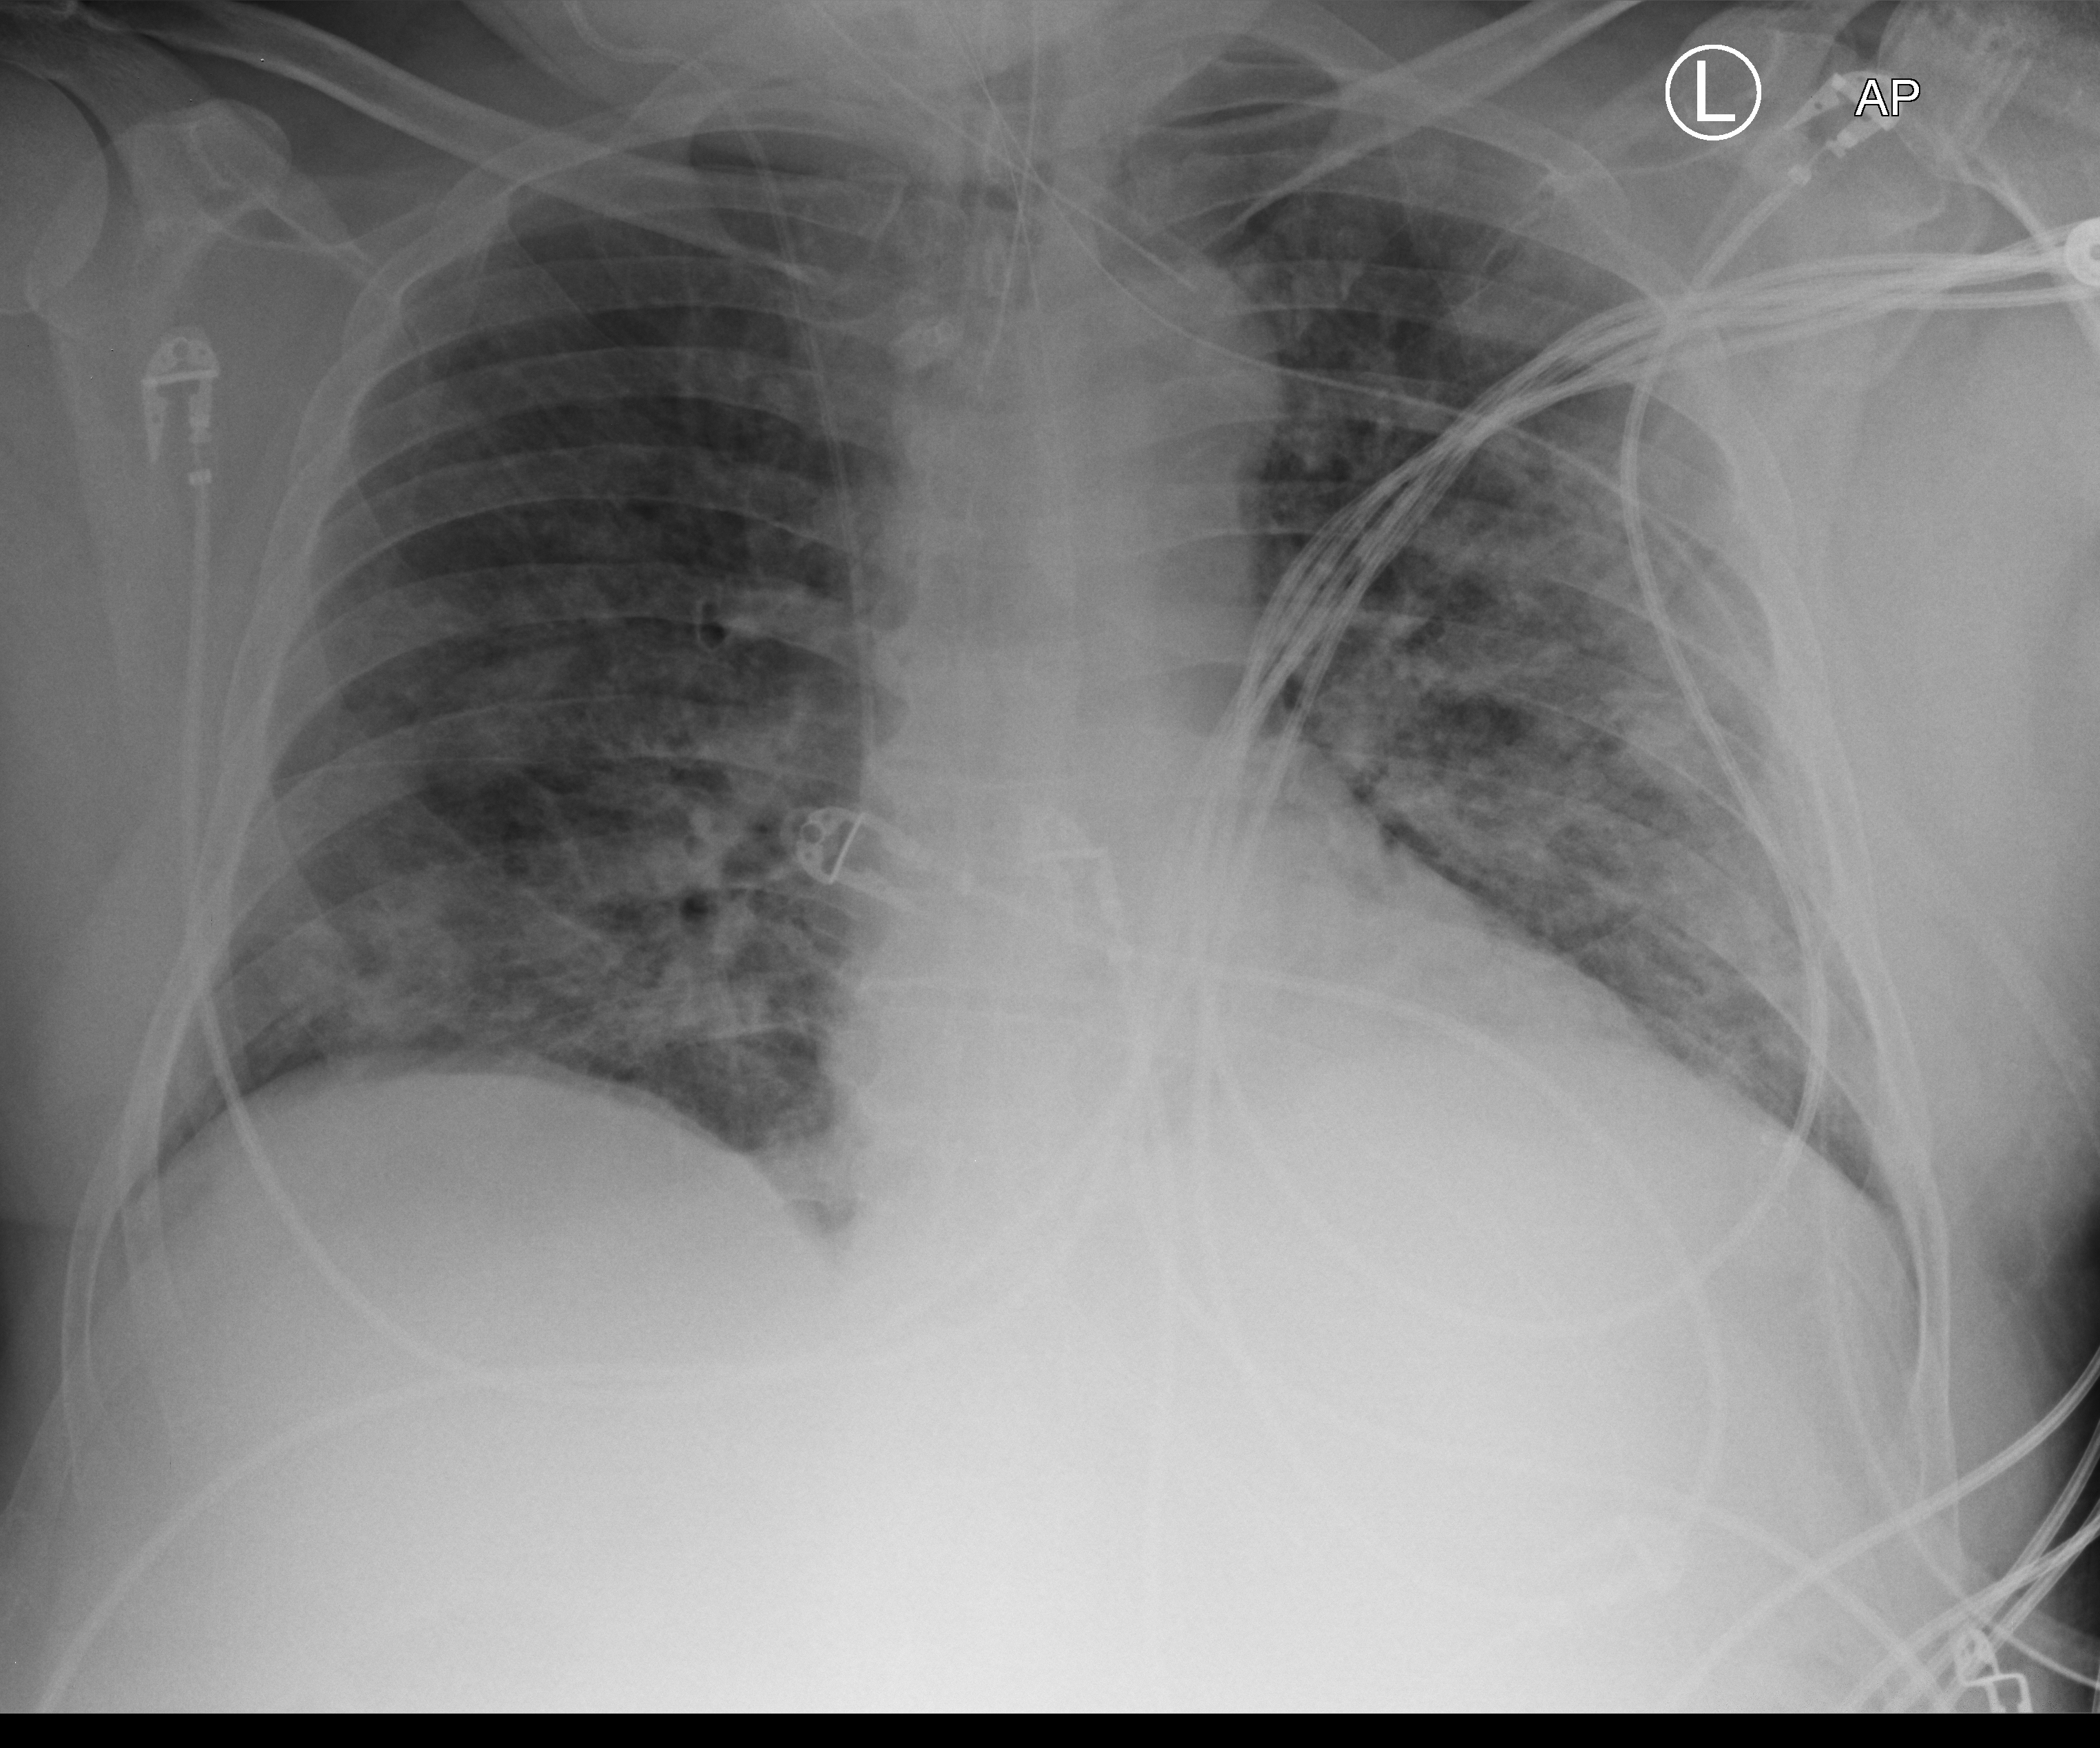
Bedside chest radiograph (computed radiography), anteroposterior (AP) projection. Patient hospitalised with COVID-19; male, aged 60–74 years.
Hospital-stay facts (about this admission, not read from this image; timing relative to this image not recorded): mechanically ventilated during this hospital stay: yes; length of hospital stay: 27 days; admitted to intensive care during this hospital stay: yes.